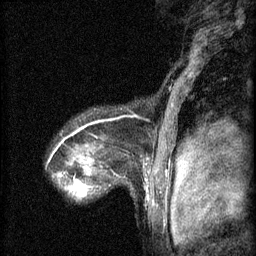
Breast MRI (dynamic contrast-enhanced), one sagittal slice; slice 50 of 60 in the series (ordered by position); 3 images stored at this slice position (order not interpretable as contrast timing); 1.5 T; TE 4.2 ms, TR 8.2 ms; 2 mm slice thickness; 256 × 256 image matrix, field of view 180 × 180 mm. Patient: female, 48 years.
Outlined on this slice (semi-automatically segmented with operator editing):
- analysis volume of interest (the breast-tissue region the enhancement analysis was run in; not a lesion): bounding box (x1, y1, x2, y2) in pixels: (60, 160, 101, 197)
- tumour enhancement mask (voxels above the 70 % enhancement threshold inside the analysis volume of interest): (71, 180, 86, 197)